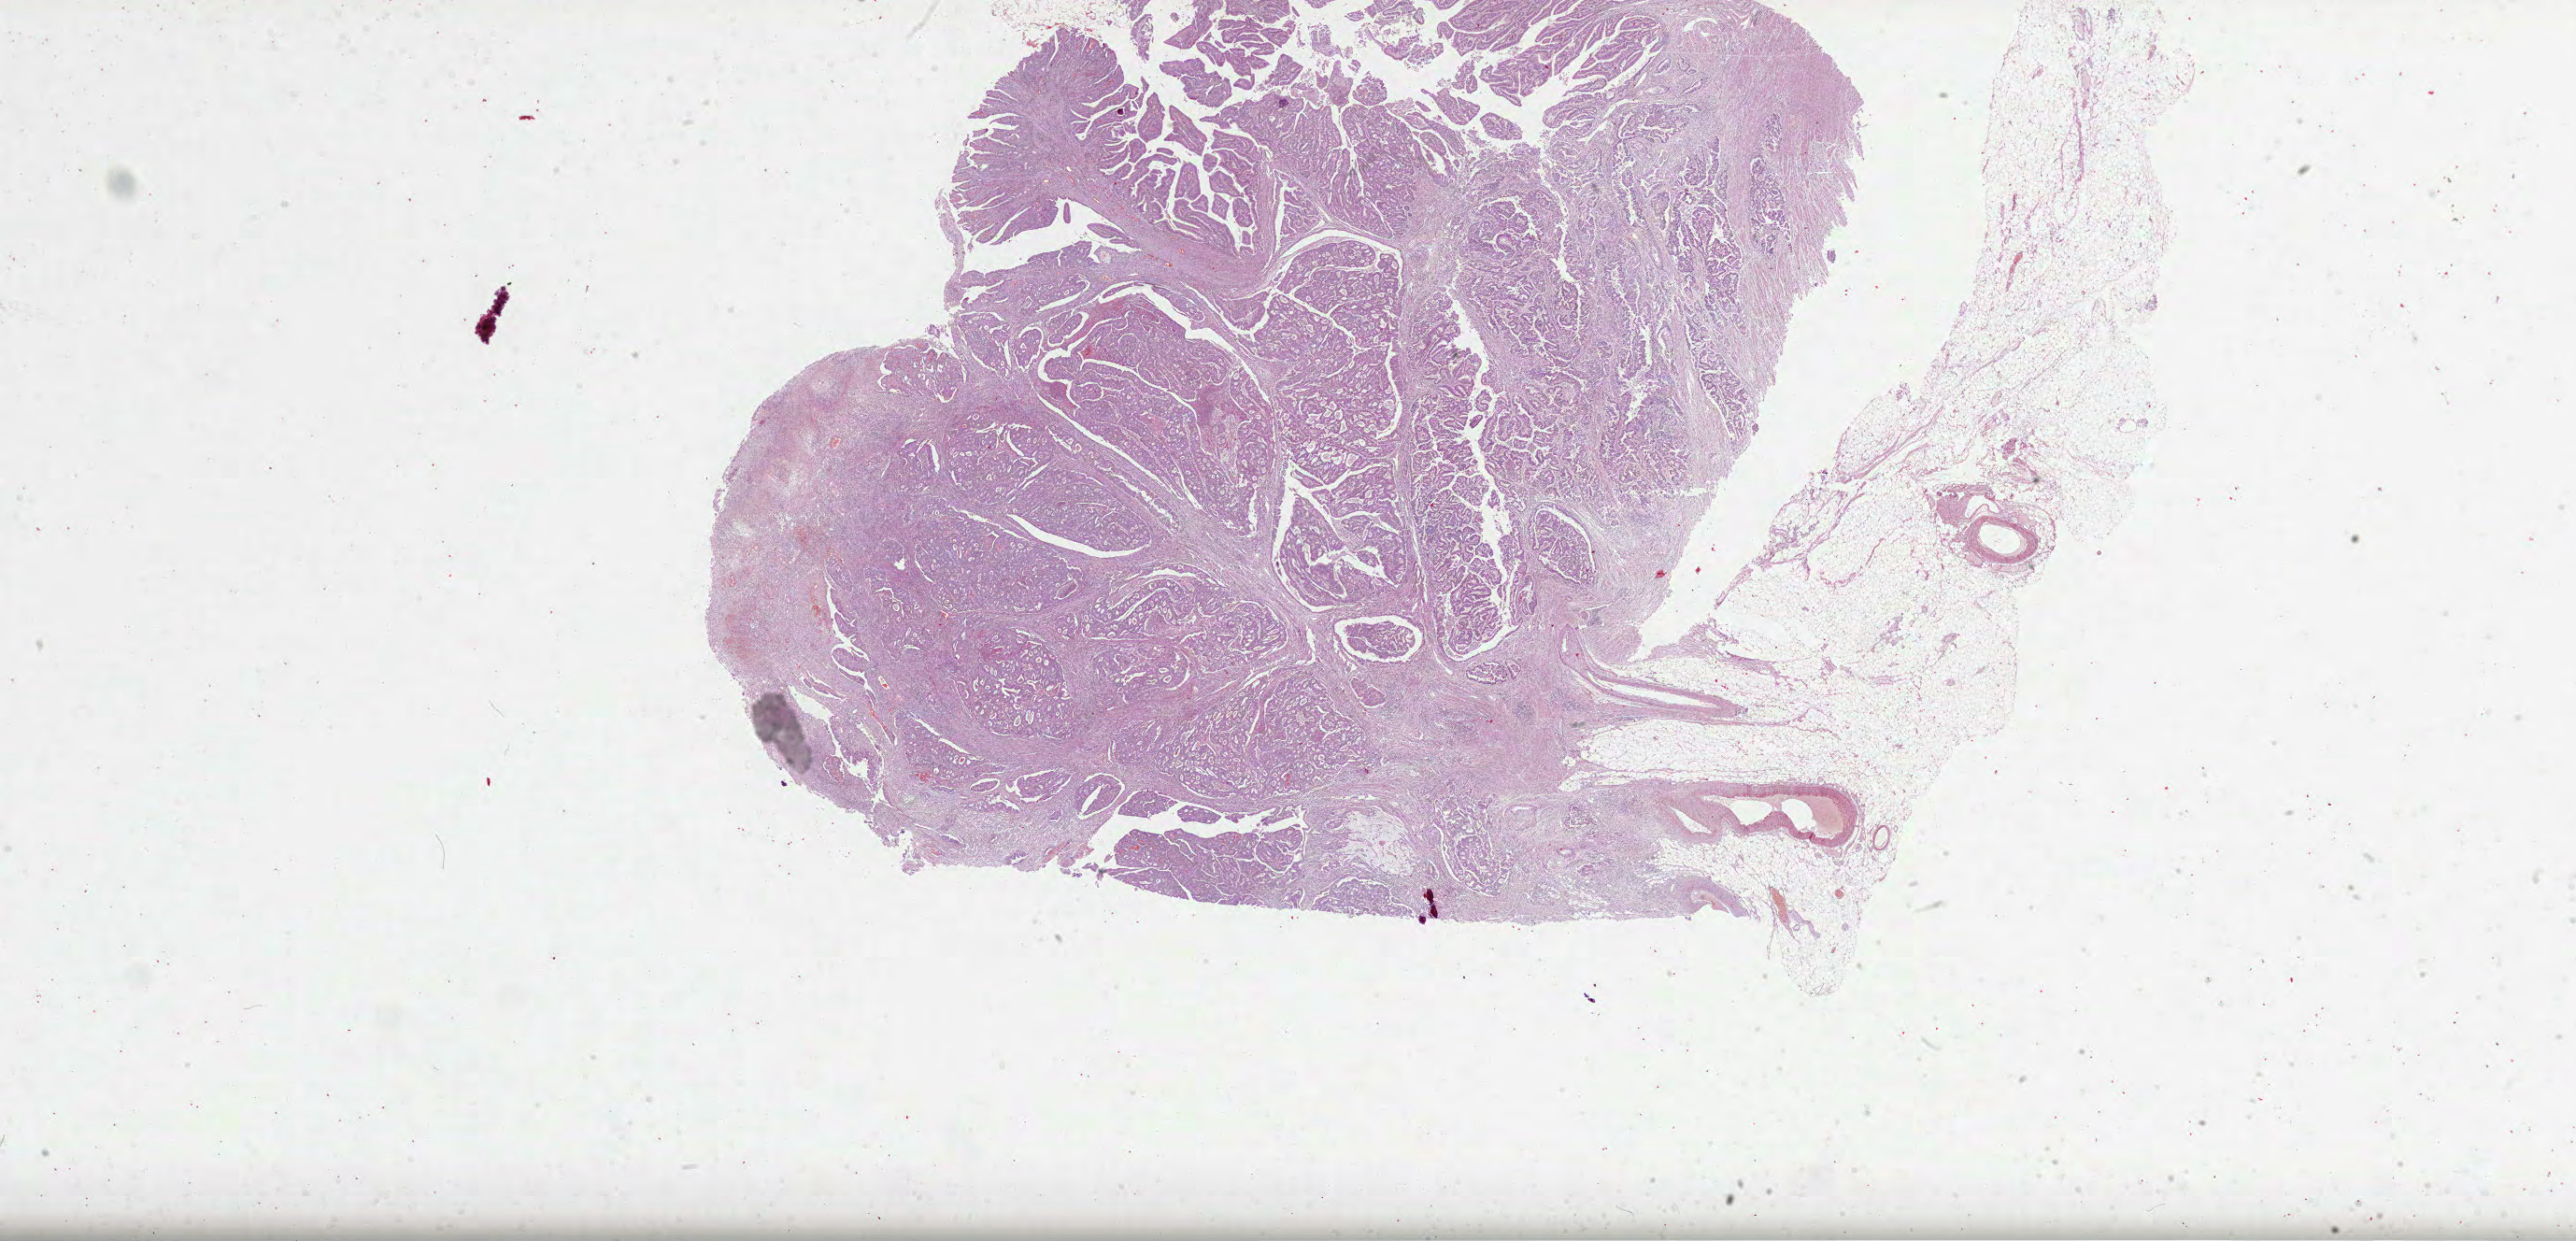
H&E-stained whole-slide image — low-resolution overview of the scanned area, about 44.5 x 21.4 mm (from a 40x scan); formalin-fixed paraffin-embedded (FFPE) diagnostic section; primary tumour sample from the colon. Male patient; age at initial diagnosis 49 years.
Pathologic diagnosis: Adenocarcinoma, NOS (splenic flexure of colon). AJCC pathologic stage: IIA.